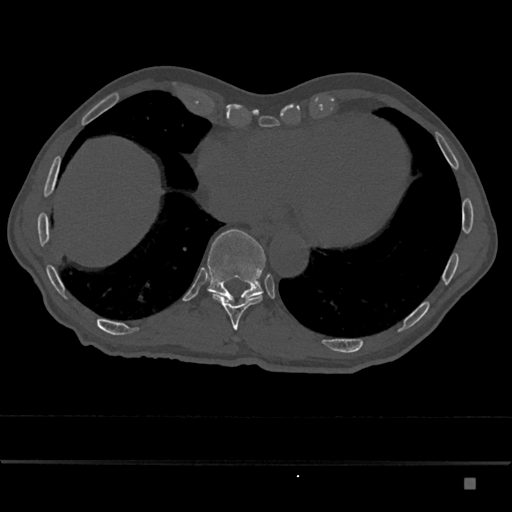
CT including the spine, one axial slice. Position 716 of 797 along the scan axis. Bone window (W 1800 / L 400 HU). 0.5 mm slice thickness. 512 × 512 image matrix, field of view 390 × 390 mm. Patient: male, 72 years. Case-level facts recorded for this patient, not image findings: primary cancer: prostate.
Structures marked on this image (semi-automatically segmented with operator editing):
- T10 vertebra: bounding box (x1, y1, x2, y2) in pixels: (213, 293, 262, 330)
- T11 vertebra: (207, 229, 266, 302)